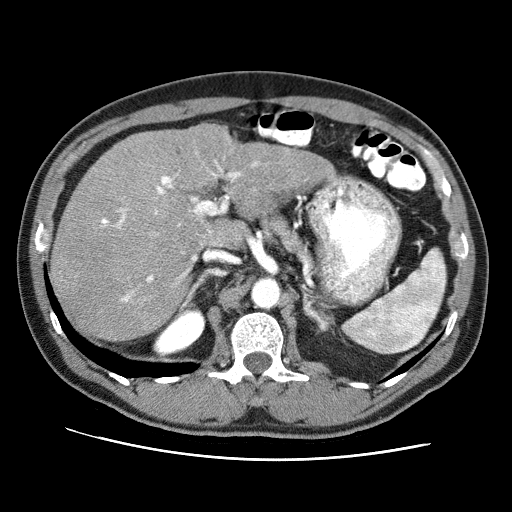
Contrast-enhanced abdominal CT (liver protocol), one axial slice. Slice 47 of 71 in the series (ordered by position). Reconstruction kernel STANDARD. 120 kVp. Soft-tissue window (W 400 / L 40 HU). 512 × 512 image matrix, field of view 360 × 360 mm. Case-level facts recorded for this patient, not image findings: diagnosis: hepatocellular carcinoma (patient treated with transarterial chemoembolisation; whether this scan precedes or follows treatment is not stated here); TNM stage (as recorded): Stage-II; Child-Pugh class: A.
Outlined on this slice (semi-automatic segmentation, software-assisted and operator-edited):
- liver parenchyma outside the tumour (the mass and vessels are separate outlines, so this box may not span the whole liver): bounding box (x1, y1, x2, y2) in pixels: (50, 124, 334, 342)
- liver vessels: (101, 163, 257, 301)